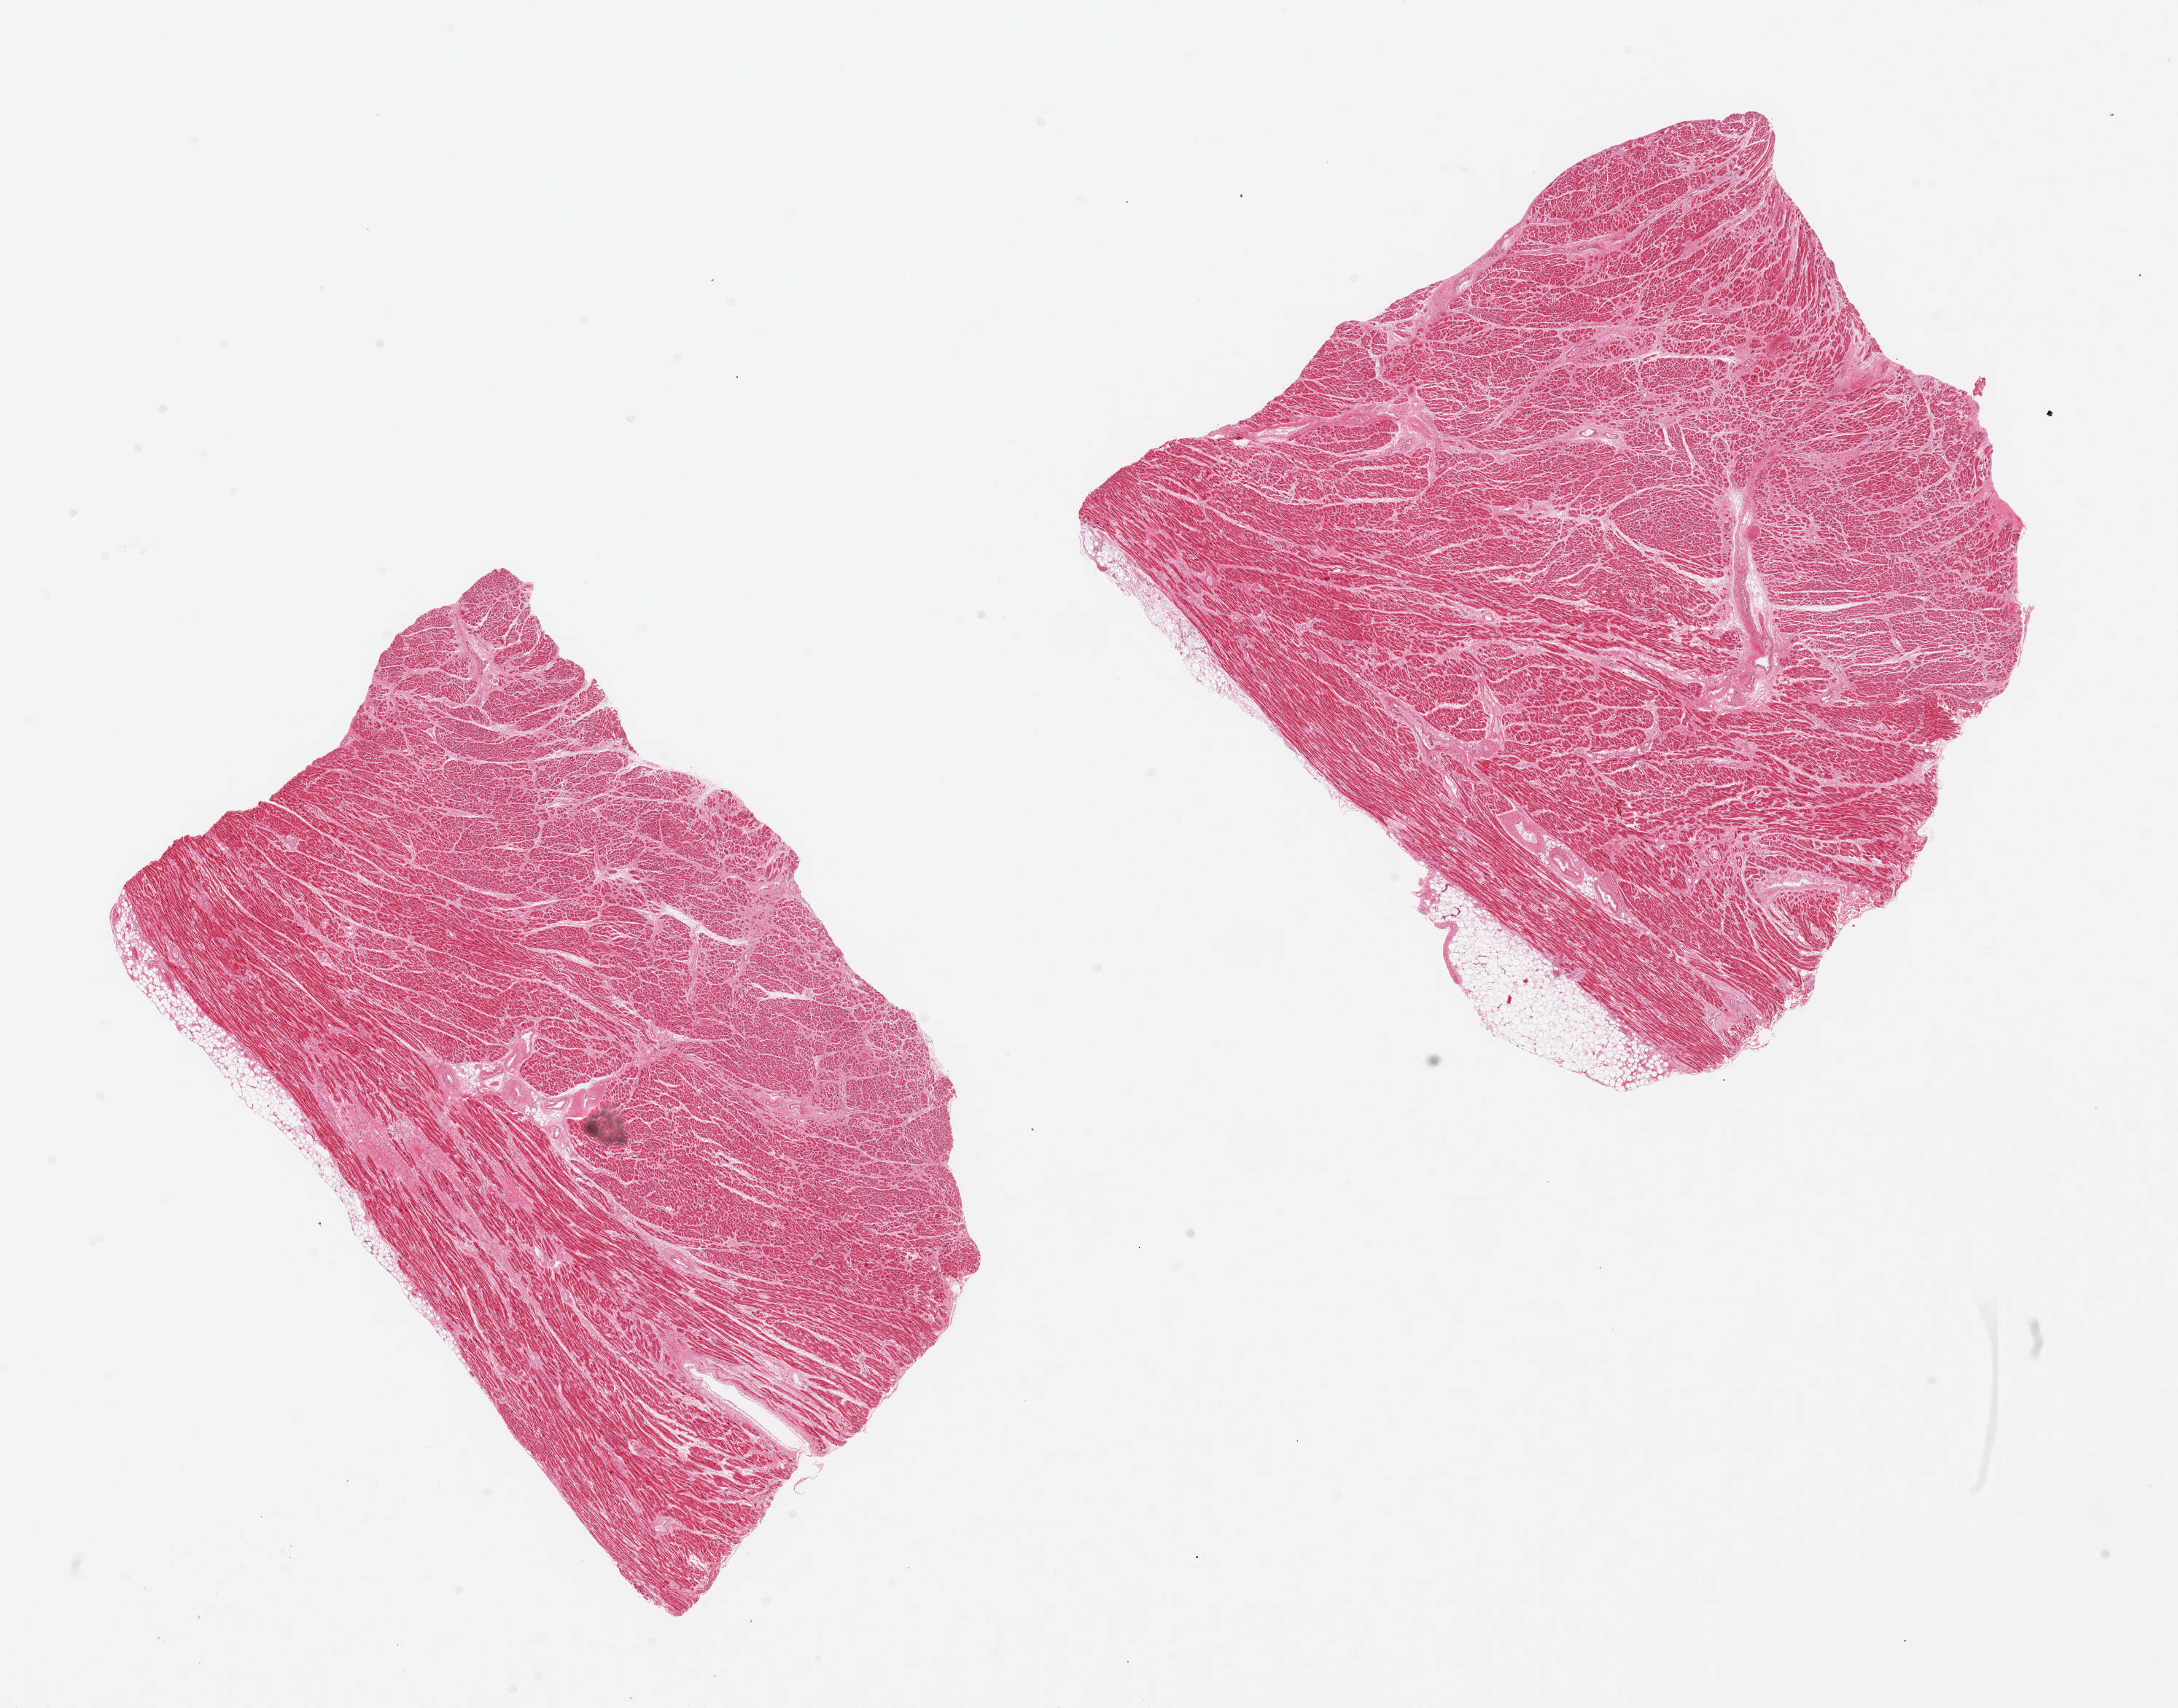
Haematoxylin and eosin whole-slide image, shown as a low-resolution overview of the whole scanned area (about 23.6 x 18.5 mm, acquisition: 20x scan). PAXgene-fixed paraffin-embedded (PFPE) section. Section of heart (target tissue). Donor tissue sample. Donor sex: male.
Pathologist's review note for this sample: 2 pieces; patchy scars (largest) & muscle drop-out consistent with old ischemia; thin layer of pericardial fat.